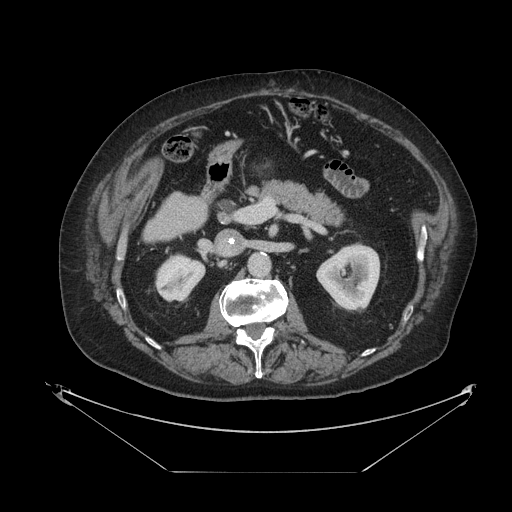
Contrast-enhanced abdominal CT, one axial slice; position 40 of 121 along the scan axis; reconstruction kernel STANDARD; 120 kVp; intravenous contrast given; soft-tissue window (W 400 / L 40 HU); 2.5 mm slice thickness; 512 × 512 image matrix, field of view 500 × 500 mm. Male patient, age 68 years. Case-level facts recorded for this patient, not image findings: diagnosis: colorectal cancer liver metastases, imaged before liver resection; multiple liver metastases: no; largest metastasis: 4 cm; chemotherapy before resection: yes.
Annotated regions visible in this slice (outlined manually by an expert reader):
- liver: bounding box [x1, y1, x2, y2] px = [147, 194, 207, 239]
- planned liver remnant (the part of the liver to remain after resection): [147, 193, 207, 240]